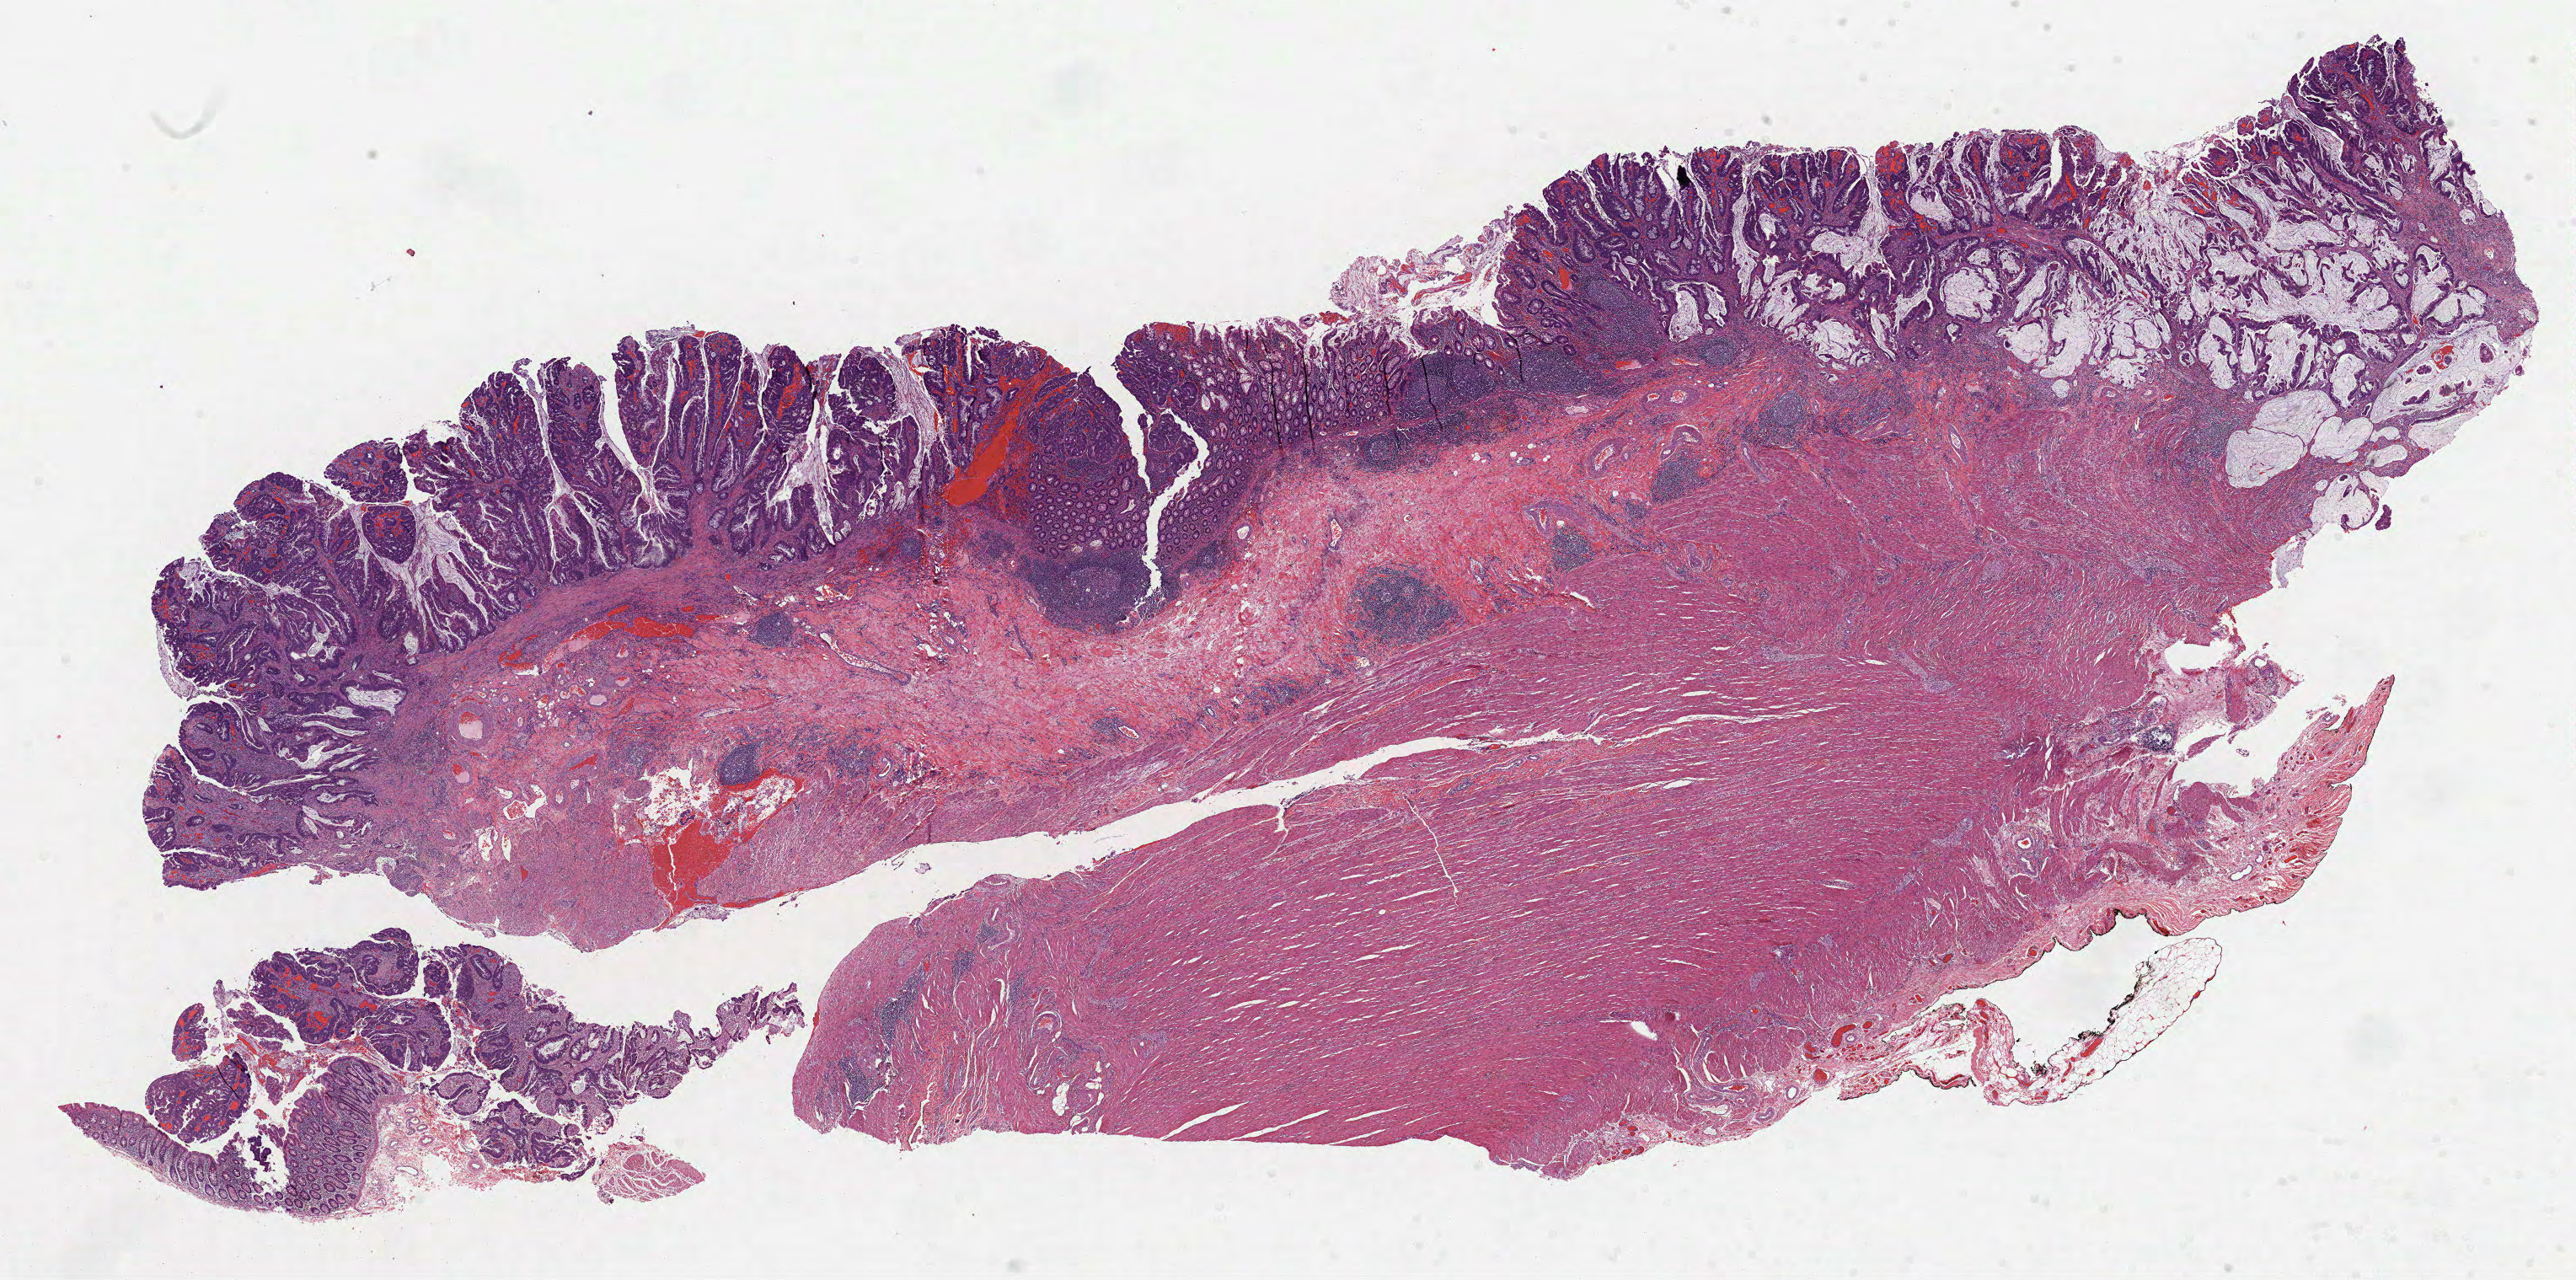
Whole-slide histology image, H&E, shown as a low-resolution overview of the whole scanned area (about 24.7 x 12.3 mm, acquisition: 40x scan); formalin-fixed paraffin-embedded (FFPE) diagnostic section; primary tumour sample from the colon. Female patient.
Histologic diagnosis: Mucinous adenocarcinoma. AJCC pathologic stage: I. TNM: T2 N0 MX.